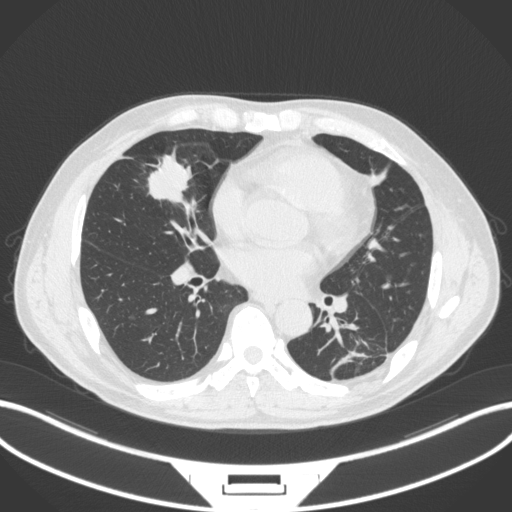
Chest CT, one axial slice; 120 kVp; lung window (W 1500 / L -600 HU); 1 mm slice thickness; 512 × 512 image matrix, field of view 400 × 400 mm. Male patient, age 59 years. Case-level facts recorded for this patient, not image findings: clinical TNM (as recorded): T2a N1 M0.
Structures marked on this image (rectangle marked by the reading radiologist):
- lung tumour (recorded histology: adenocarcinoma): box from (x=143, y=149) to (x=197, y=207) px